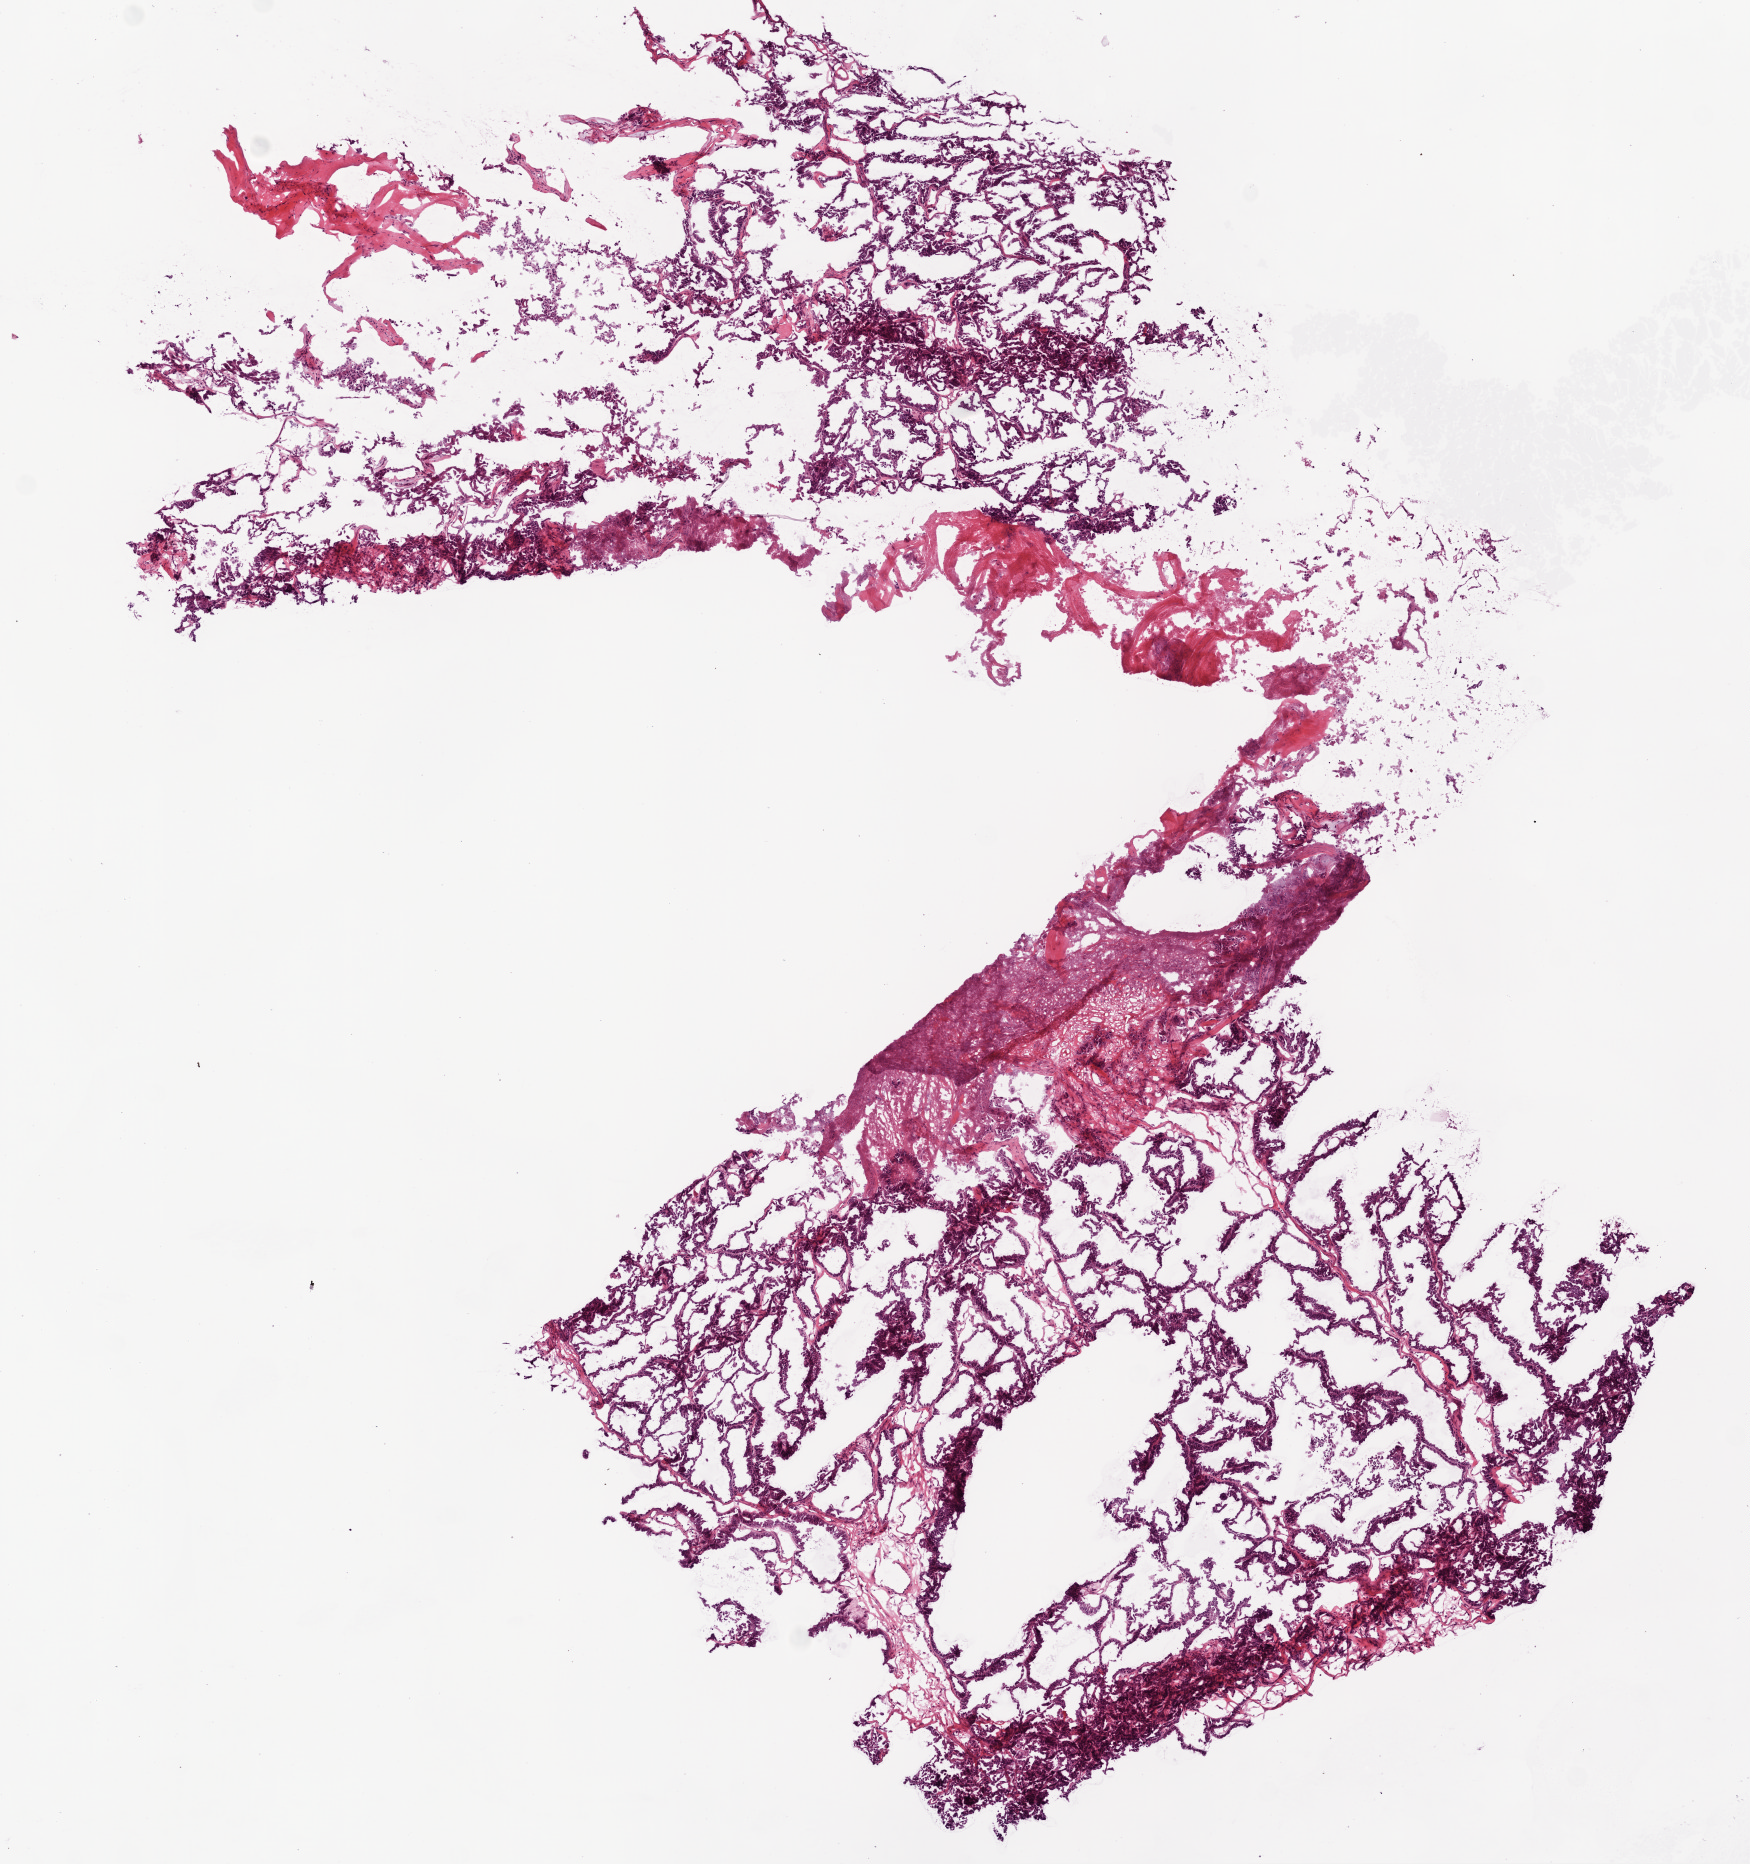
Digitized H&E-stained tissue section (whole slide), low-resolution overview of the scanned area, about 7.0 x 7.5 mm. Frozen section. Sample: primary tumour, ovary. Female, age 57 years at initial diagnosis. Histologic grade: G2 (moderately differentiated). Composition of this section per pathologist review: tumour cells 85%, tumour nuclei 90%, normal cells 0%, stromal cells 0%, necrosis 15%.
FIGO stage: IIIC. Pathologic diagnosis: Serous cystadenocarcinoma, NOS.